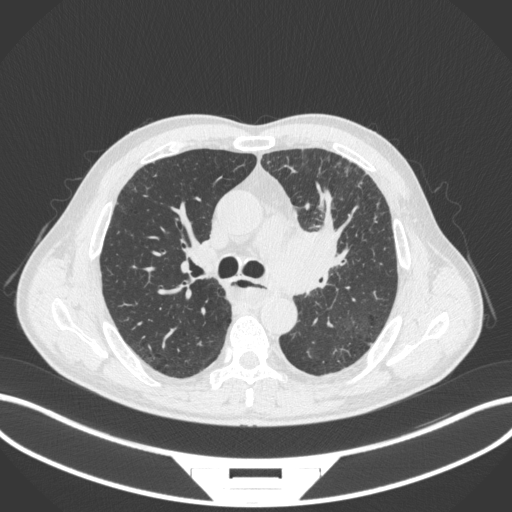
Chest CT, one axial slice. Slice 245 of 411 in the series (ordered by position). Reconstruction kernel B31f. Lung window (W 1500 / L -600 HU). 1 mm slice thickness. 512 × 512 image matrix. Patient: male, 57 years. Case-level facts recorded for this patient, not image findings: clinical TNM (as recorded): T2a N1 M0.
Outlined on this slice (bounding box drawn by a radiologist):
- lung tumour (recorded histology: squamous cell carcinoma): bounding box [x1, y1, x2, y2] px = [266, 218, 347, 300]